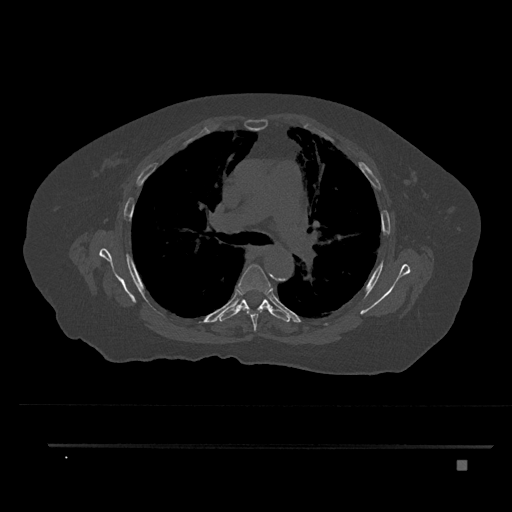
CT including the spine, one axial slice. Position 548 of 797 along the scan axis. Reconstruction kernel Br40s/3. Bone window (W 1800 / L 400 HU). 0.5 mm slice thickness. 512 × 512 image matrix. Female patient, age 76 years. From the clinical record (not read from this slice): primary cancer: lung.
Annotated regions visible in this slice (semi-automatically segmented with operator editing):
- T5 vertebra: bounding box (x1, y1, x2, y2) in pixels: (238, 264, 271, 331)
- T6 vertebra: (219, 289, 290, 322)